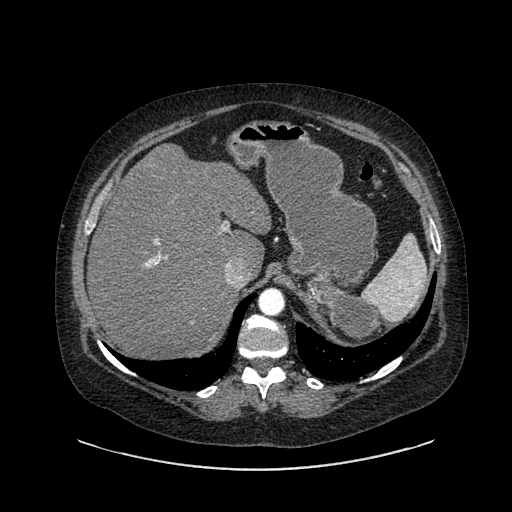
Contrast-enhanced abdominal CT, one axial slice. Slice 632 of 769 in the series (ordered by position). Reconstruction kernel SOFT. 120 kVp. Intravenous contrast given. Soft-tissue window (W 400 / L 40 HU). 0.62 mm slice thickness. 512 × 512 image matrix. Patient: female, 61 years. Case-level facts recorded for this patient, not image findings: diagnosis: adrenocortical carcinoma; tumour side: left adrenal; tumour size at pathology: 13 cm; Ki-67 index: 79 %; stage (as recorded): 2.
Annotated regions visible in this slice (semi-automatically segmented with operator editing):
- mass: bounding box (x1, y1, x2, y2) in pixels: (311, 274, 376, 343)